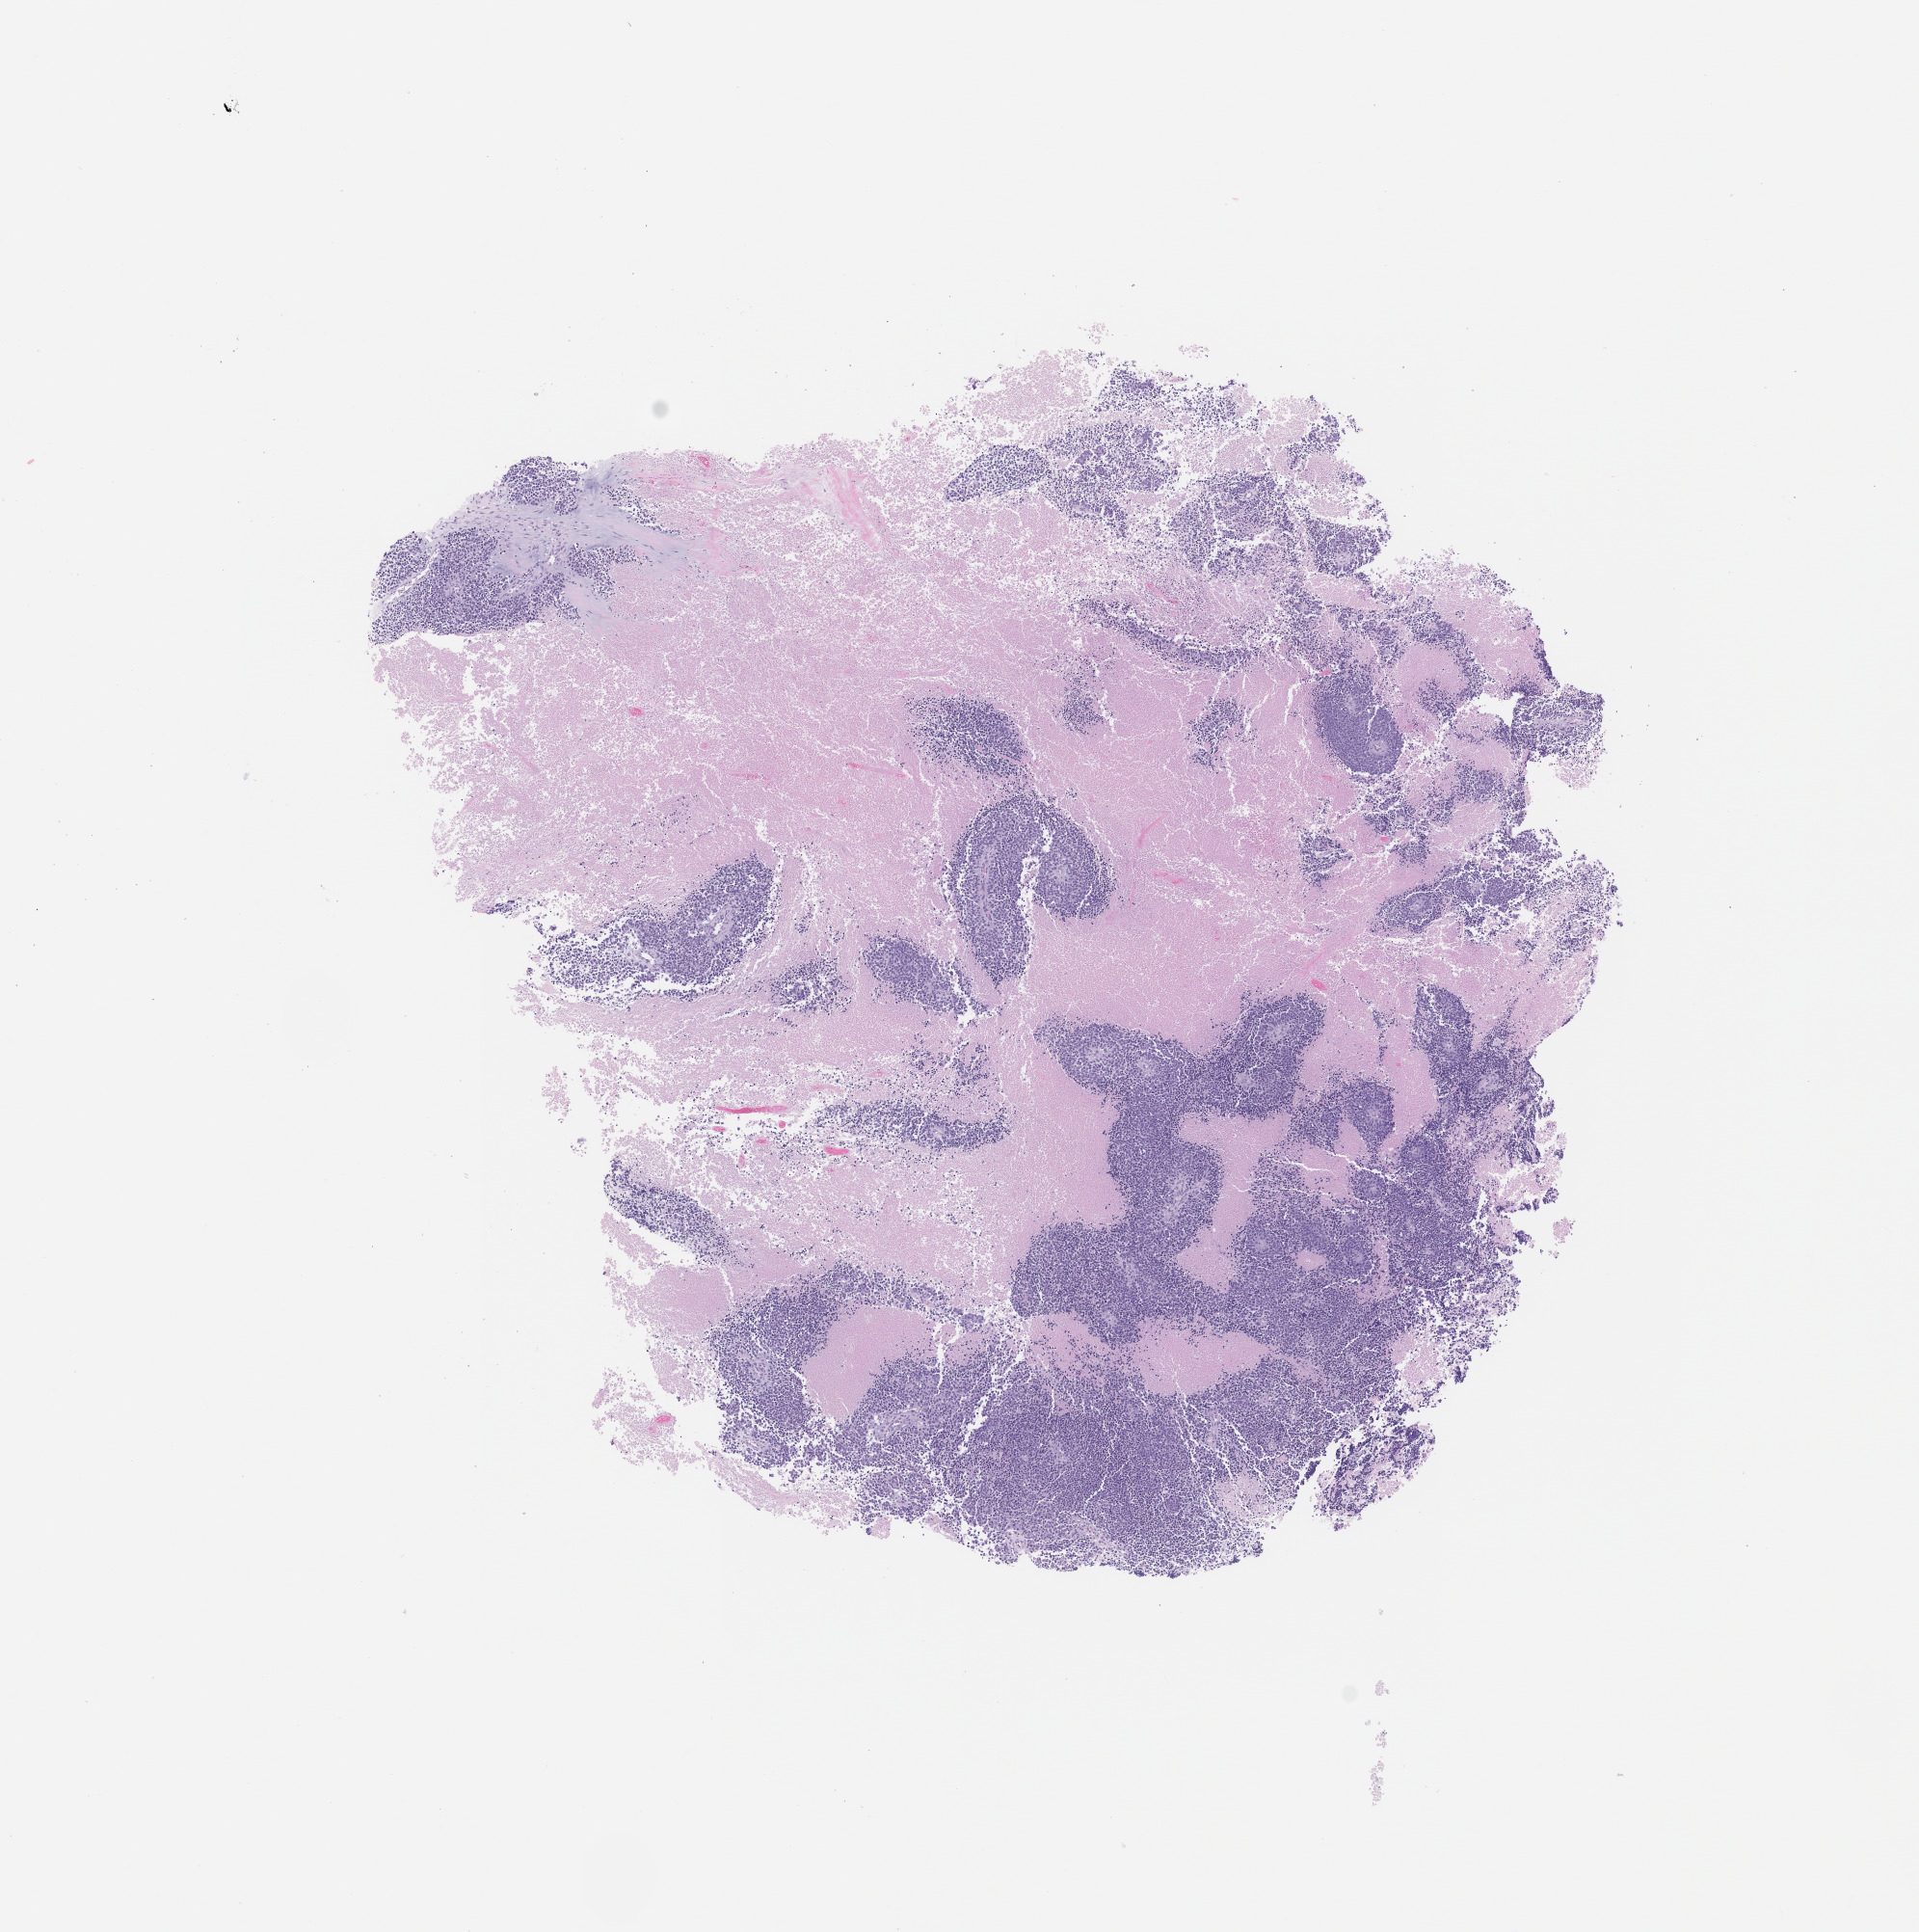
Whole-slide image, hematoxylin and eosin (H&E) stain of the patient's (originator) tumor tissue — a low-resolution overview of the entire scanned area, about 8.0 x 8.0 mm, formalin-fixed, paraffin-embedded (FFPE) tissue, originating tumor site category: lung. Male patient.
Diagnosis: Lung Adenocarcinoma.